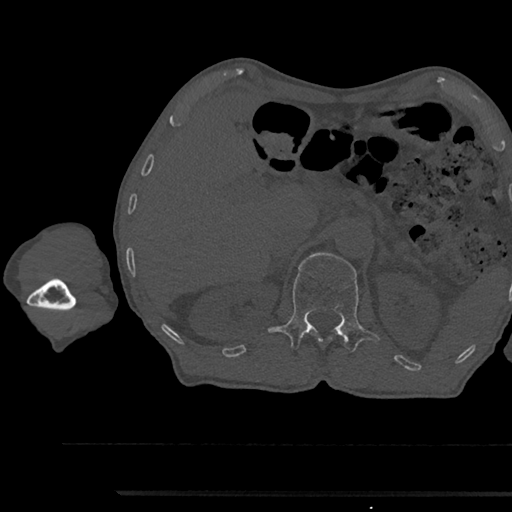
CT including the spine, one axial slice; slice 658 of 797 in the series (ordered by position); reconstruction kernel Br40s/3; 120 kVp; bone window (W 1800 / L 400 HU); 0.5 mm slice thickness; 512 × 512 image matrix, field of view 367 × 367 mm. Patient: male, 79 years. Case-level facts recorded for this patient, not image findings: primary cancer: prostate.
Annotated regions visible in this slice (semi-automatically segmented with operator editing):
- L1 vertebra: bounding box (x1, y1, x2, y2) in pixels: (267, 252, 380, 352)